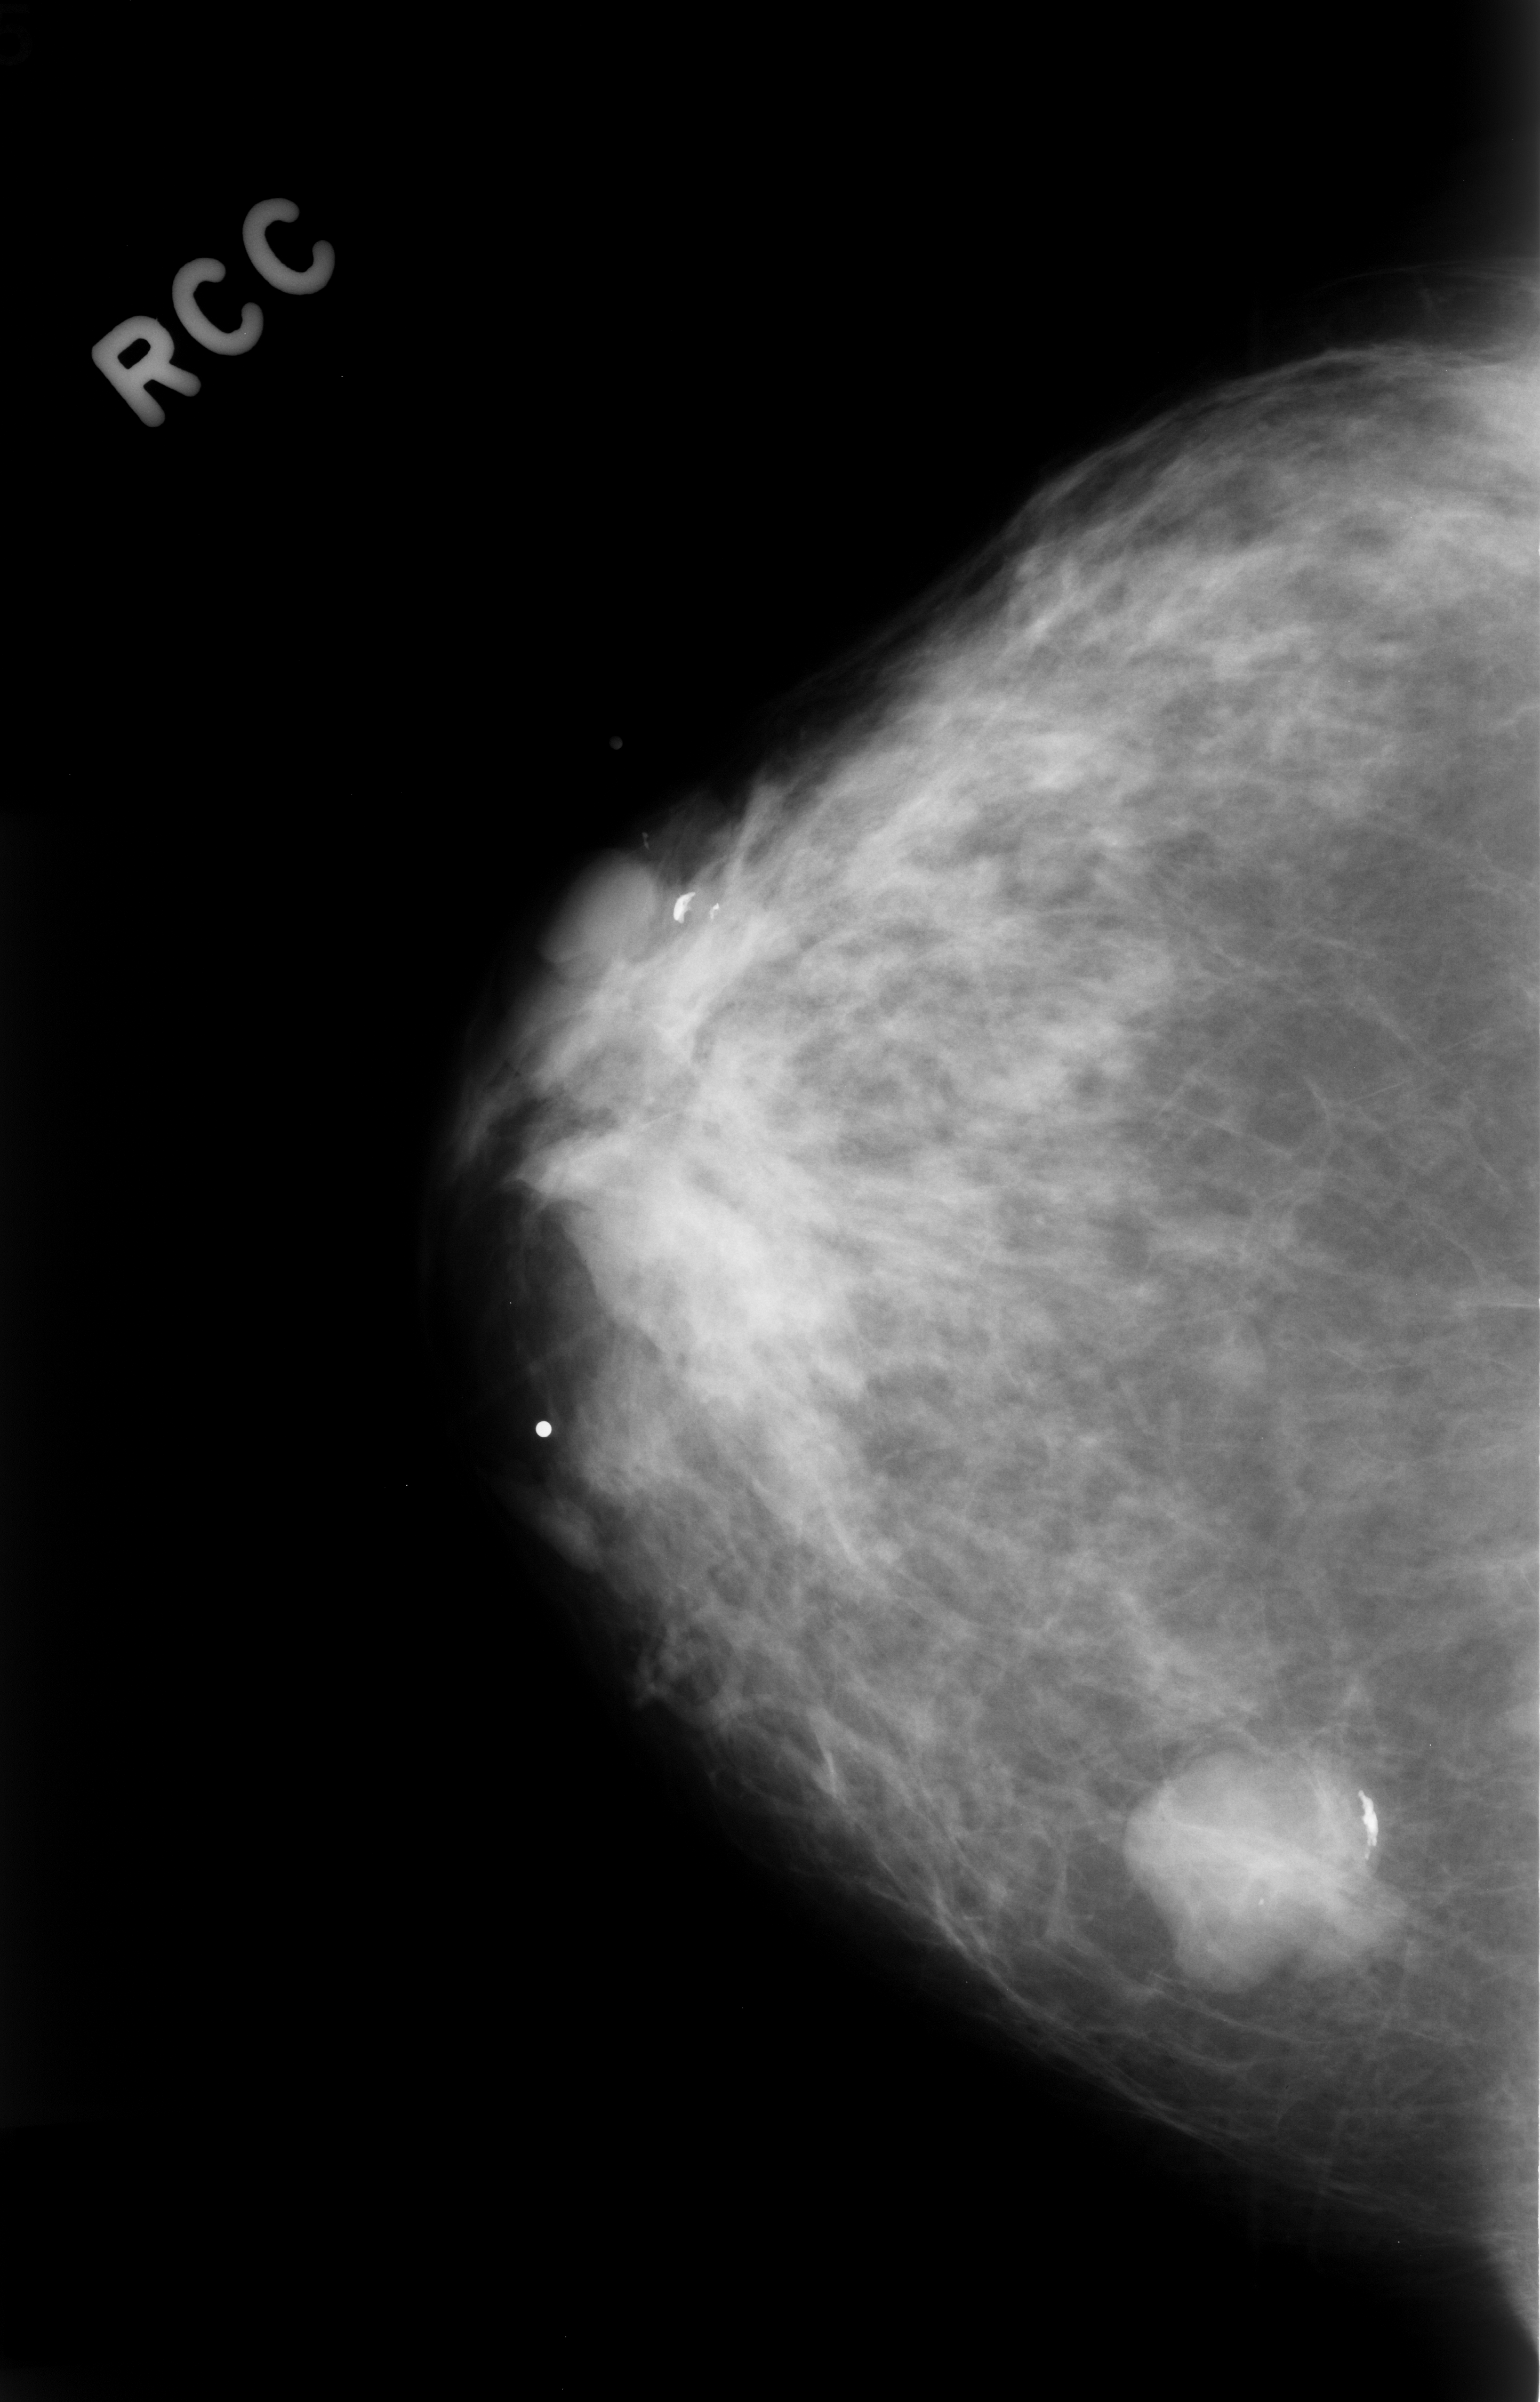
Mammogram (digitized film); right breast; craniocaudal (CC) view; BI-RADS breast density category 2 (scale 1–4); 1540 × 2402 image matrix.
Expert-marked regions of interest on this image (one box per marked abnormality):
- Finding 1 of 4: mass, shape oval, margins circumscribed; BI-RADS assessment category 3; pathology result (as recorded, not read from the image): benign: box from (x=536, y=1499) to (x=601, y=1568) px
- Finding 2 of 4: mass, shape oval, margins circumscribed; BI-RADS assessment category 3; pathology (as recorded): benign: (x=546, y=853)–(x=657, y=973)
- Finding 3 of 4: mass, shape oval, margins circumscribed; BI-RADS assessment category 3; pathology result (as recorded, not read from the image): benign: (x=565, y=1138)–(x=757, y=1285)
- Finding 4 of 4: mass, shape lobulated, margins circumscribed; BI-RADS assessment category 3; pathology result (as recorded, not read from the image): benign: (x=1133, y=1754)–(x=1366, y=1977)